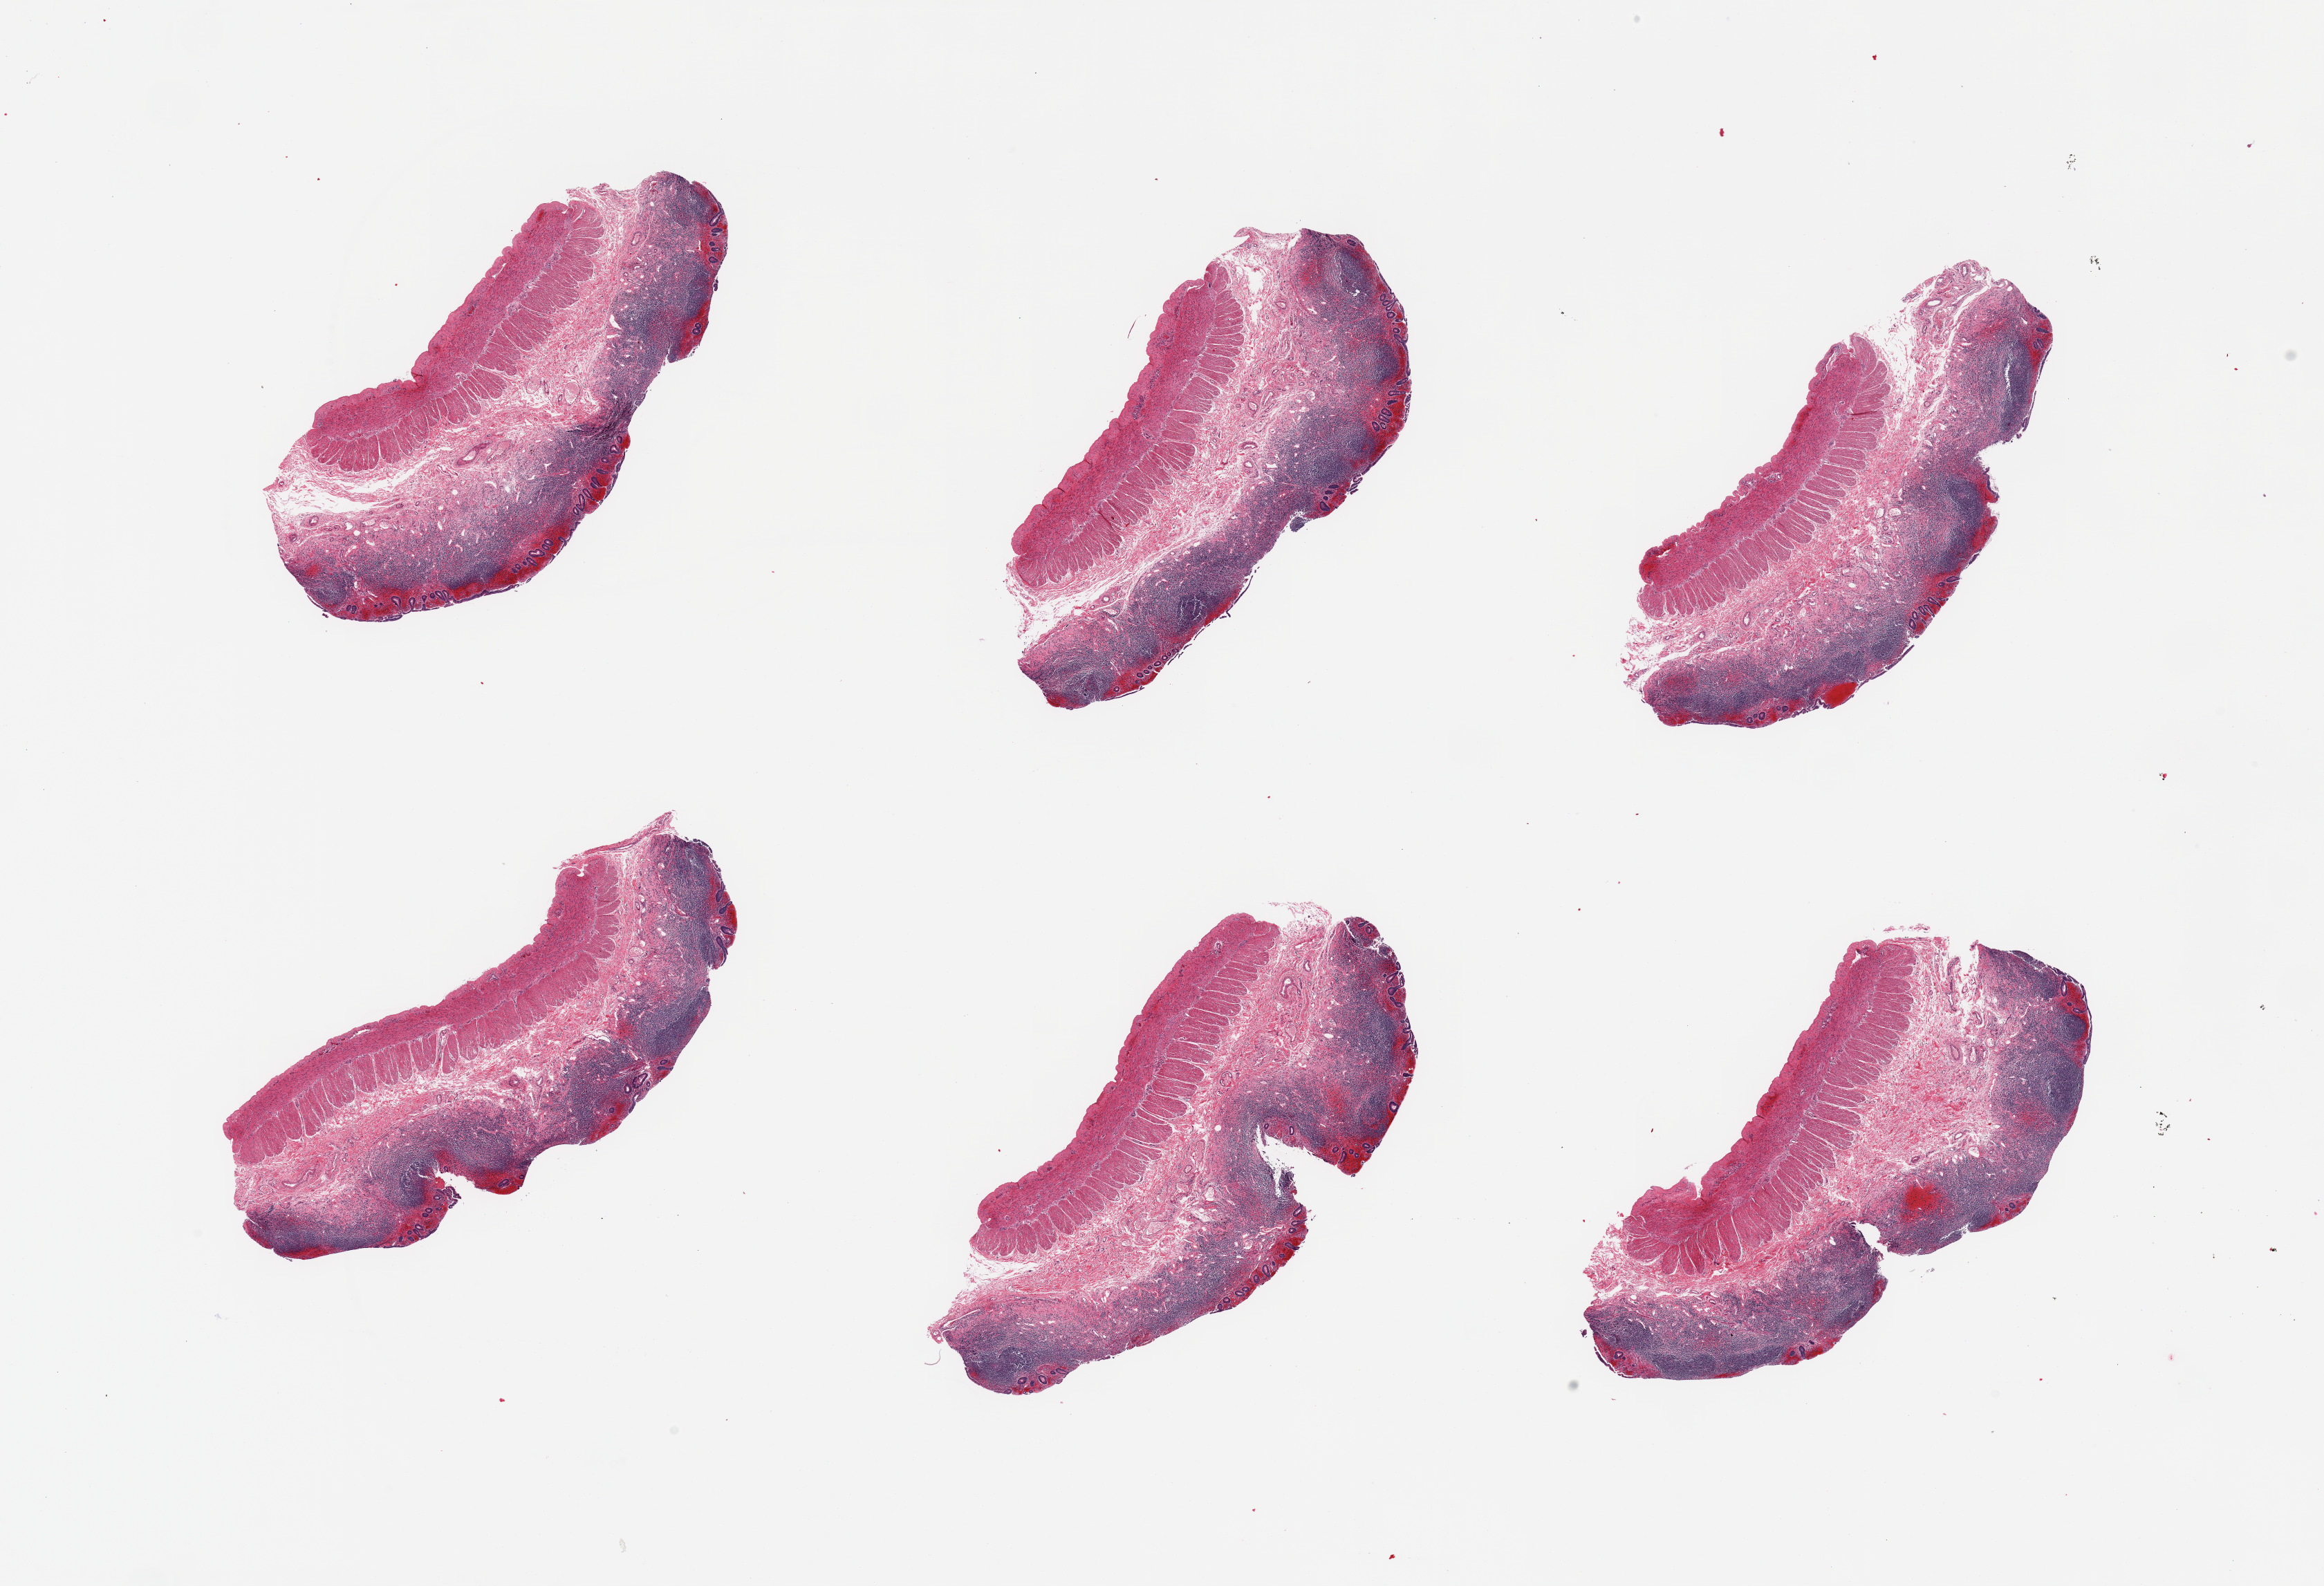
Digitized H&E-stained section, shown as a low-resolution overview of the whole scanned area (about 26.6 x 18.1 mm, acquisition: 20x scan), PAXgene-fixed paraffin-embedded (PFPE) section, sampled site (target tissue): ileum, donor tissue sample.
Pathologist's review note for this sample: 6 pieces; abundant lymphoid tissue, but muscularis propria present on all.